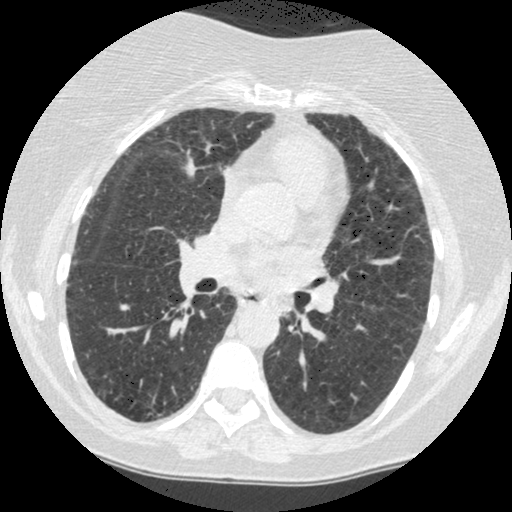
Low-dose screening chest CT, axial slice. Baseline annual screen. Lung window (W 1500 / L -600 HU). Standard (soft-tissue) reconstruction kernel (STANDARD). Slice 210 of 442 in the series. Female participant, aged 60 years at enrolment. Former smoker at enrolment.
Expert reader's lesion annotation, bounding box <264,289,307,330> (left, top, right, bottom; pixels). The screening reader recorded 2 non-calcified nodules or masses ≥4 mm on this exam (right lower lobe, left lower lobe); which of them this box marks is not recorded. Official screen result: positive, change unspecified: nodule(s) >= 4 mm or enlarging nodule(s), mass(es), or other non-specific abnormalities suspicious for lung cancer.